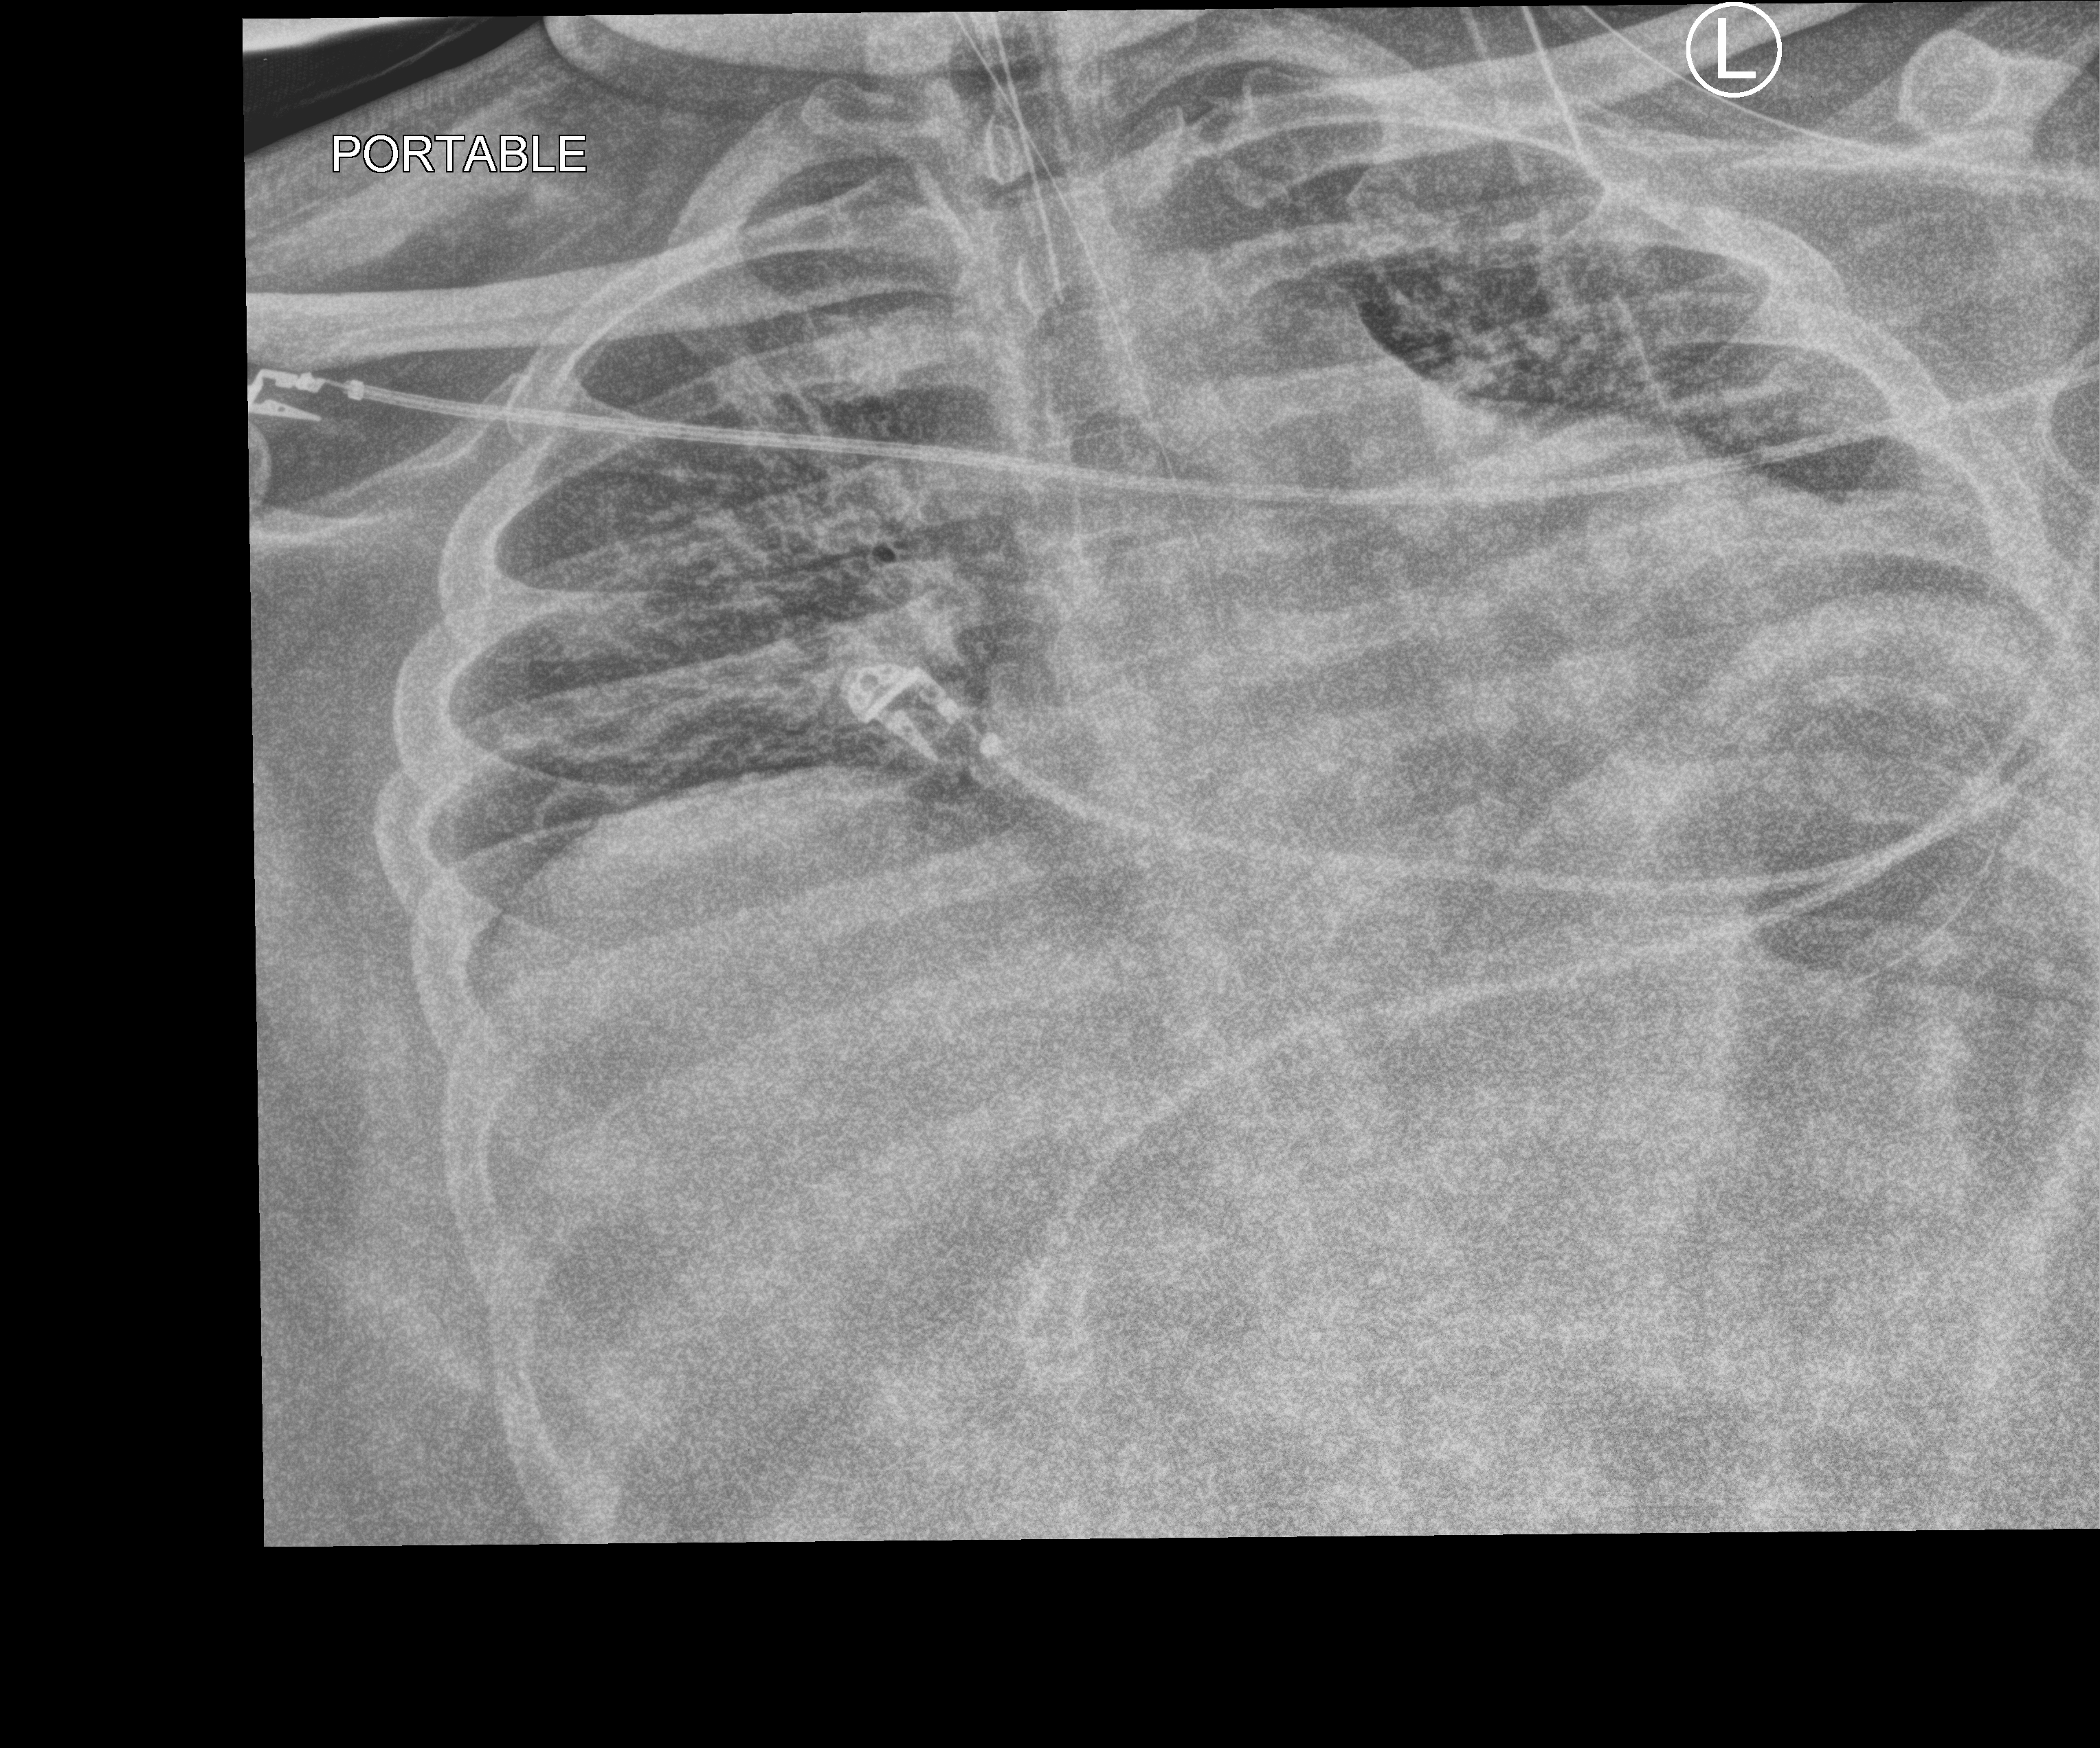
Portable chest radiograph, anteroposterior (AP) projection. Male patient hospitalised with COVID-19, age 18–59 years.
Admission-level facts for this patient (not findings on this image; timing relative to this image not recorded):
- admitted to intensive care during this hospital stay: yes
- mechanically ventilated during this hospital stay: yes
- length of hospital stay: 69 days